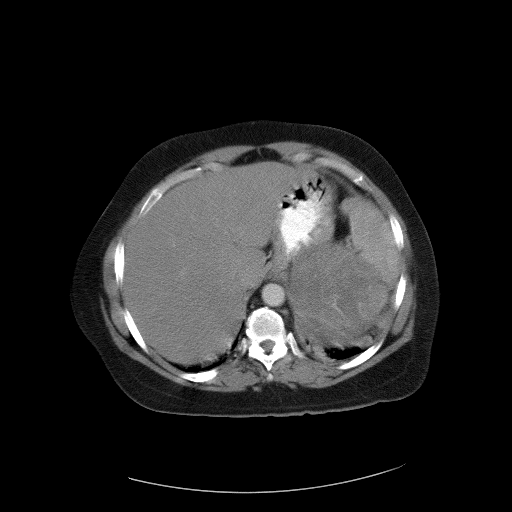
Contrast-enhanced abdominal CT, one axial slice; slice 82 of 90 in the series (ordered by position); 120 kVp; intravenous contrast given; soft-tissue window (W 400 / L 40 HU); 512 × 512 image matrix, field of view 480 × 480 mm. Female patient, age 55 years. Case-level facts recorded for this patient, not image findings: diagnosis: adrenocortical carcinoma; tumour side: left adrenal; tumour size at pathology: 22 cm; Ki-67 index: 10 %; stage (as recorded): 3.
Structures marked on this image (semi-automatically segmented with operator editing):
- mass: bounding box <290,246,385,341> (left, top, right, bottom; pixels)